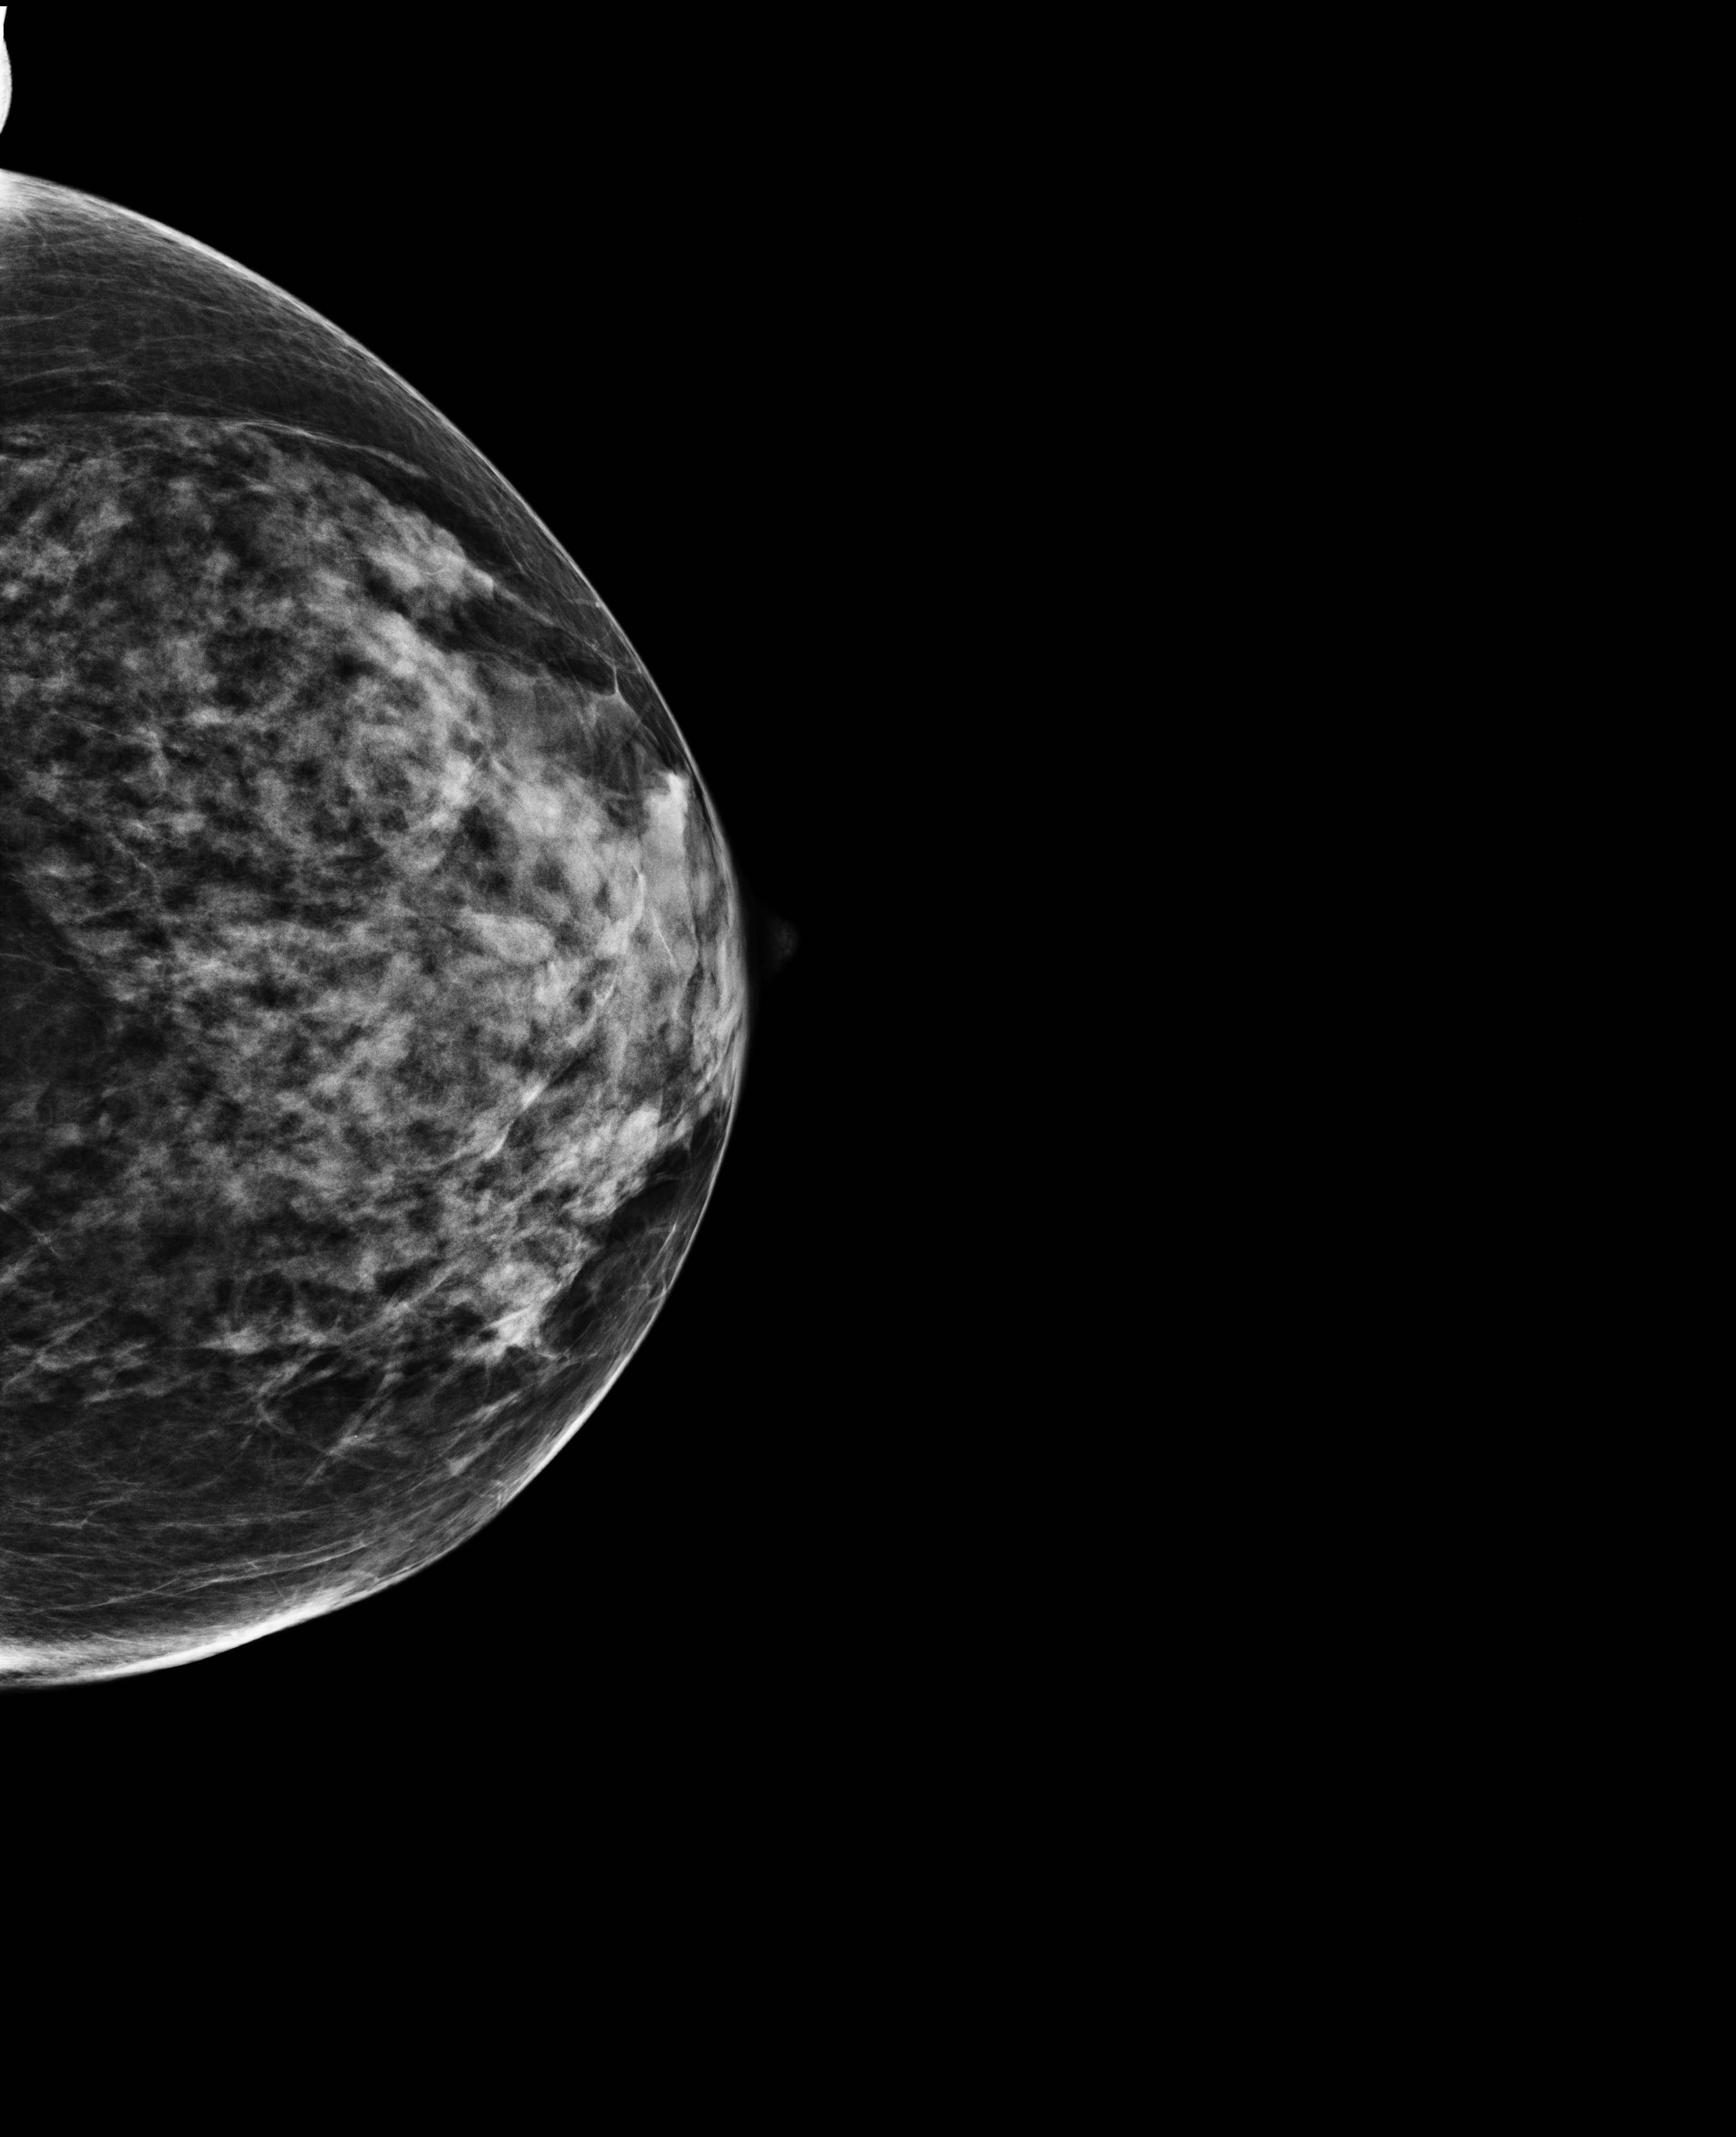
Annual screening mammography examination; system: Selenia Dimensions. Patient aged 66 years (female).
Image type: full-field digital mammogram. Breast: left. Projection: cranio-caudal projection. BI-RADS breast density category at the screening exam (both breasts, scale 1–4): 3. Final BI-RADS assessment for this screening round (tomosynthesis exam, both breasts): category 1. Recall: no recall after this screen.